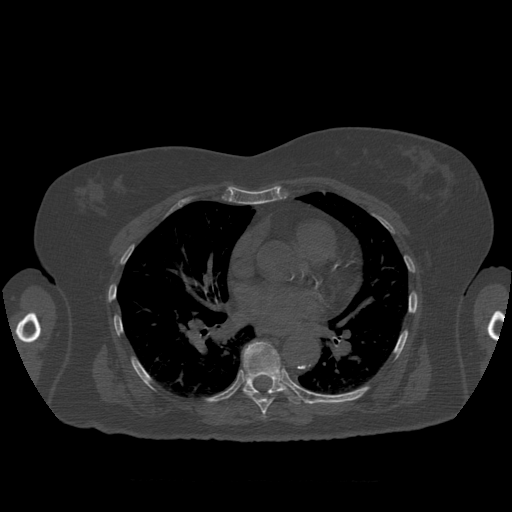
CT including the spine, one axial slice. Position 388 of 399 along the scan axis. Reconstruction kernel STANDARD. 120 kVp. Bone window (W 1800 / L 400 HU). 1.25 mm slice thickness. 512 × 512 image matrix, field of view 404 × 404 mm. Patient age 81 years. From the clinical record (not read from this slice): primary cancer: renal.
Outlined on this slice (semi-automatically segmented with operator editing):
- T7 vertebra: bounding box <244,391,275,418> (left, top, right, bottom; pixels)
- T8 vertebra: <243,342,305,405>